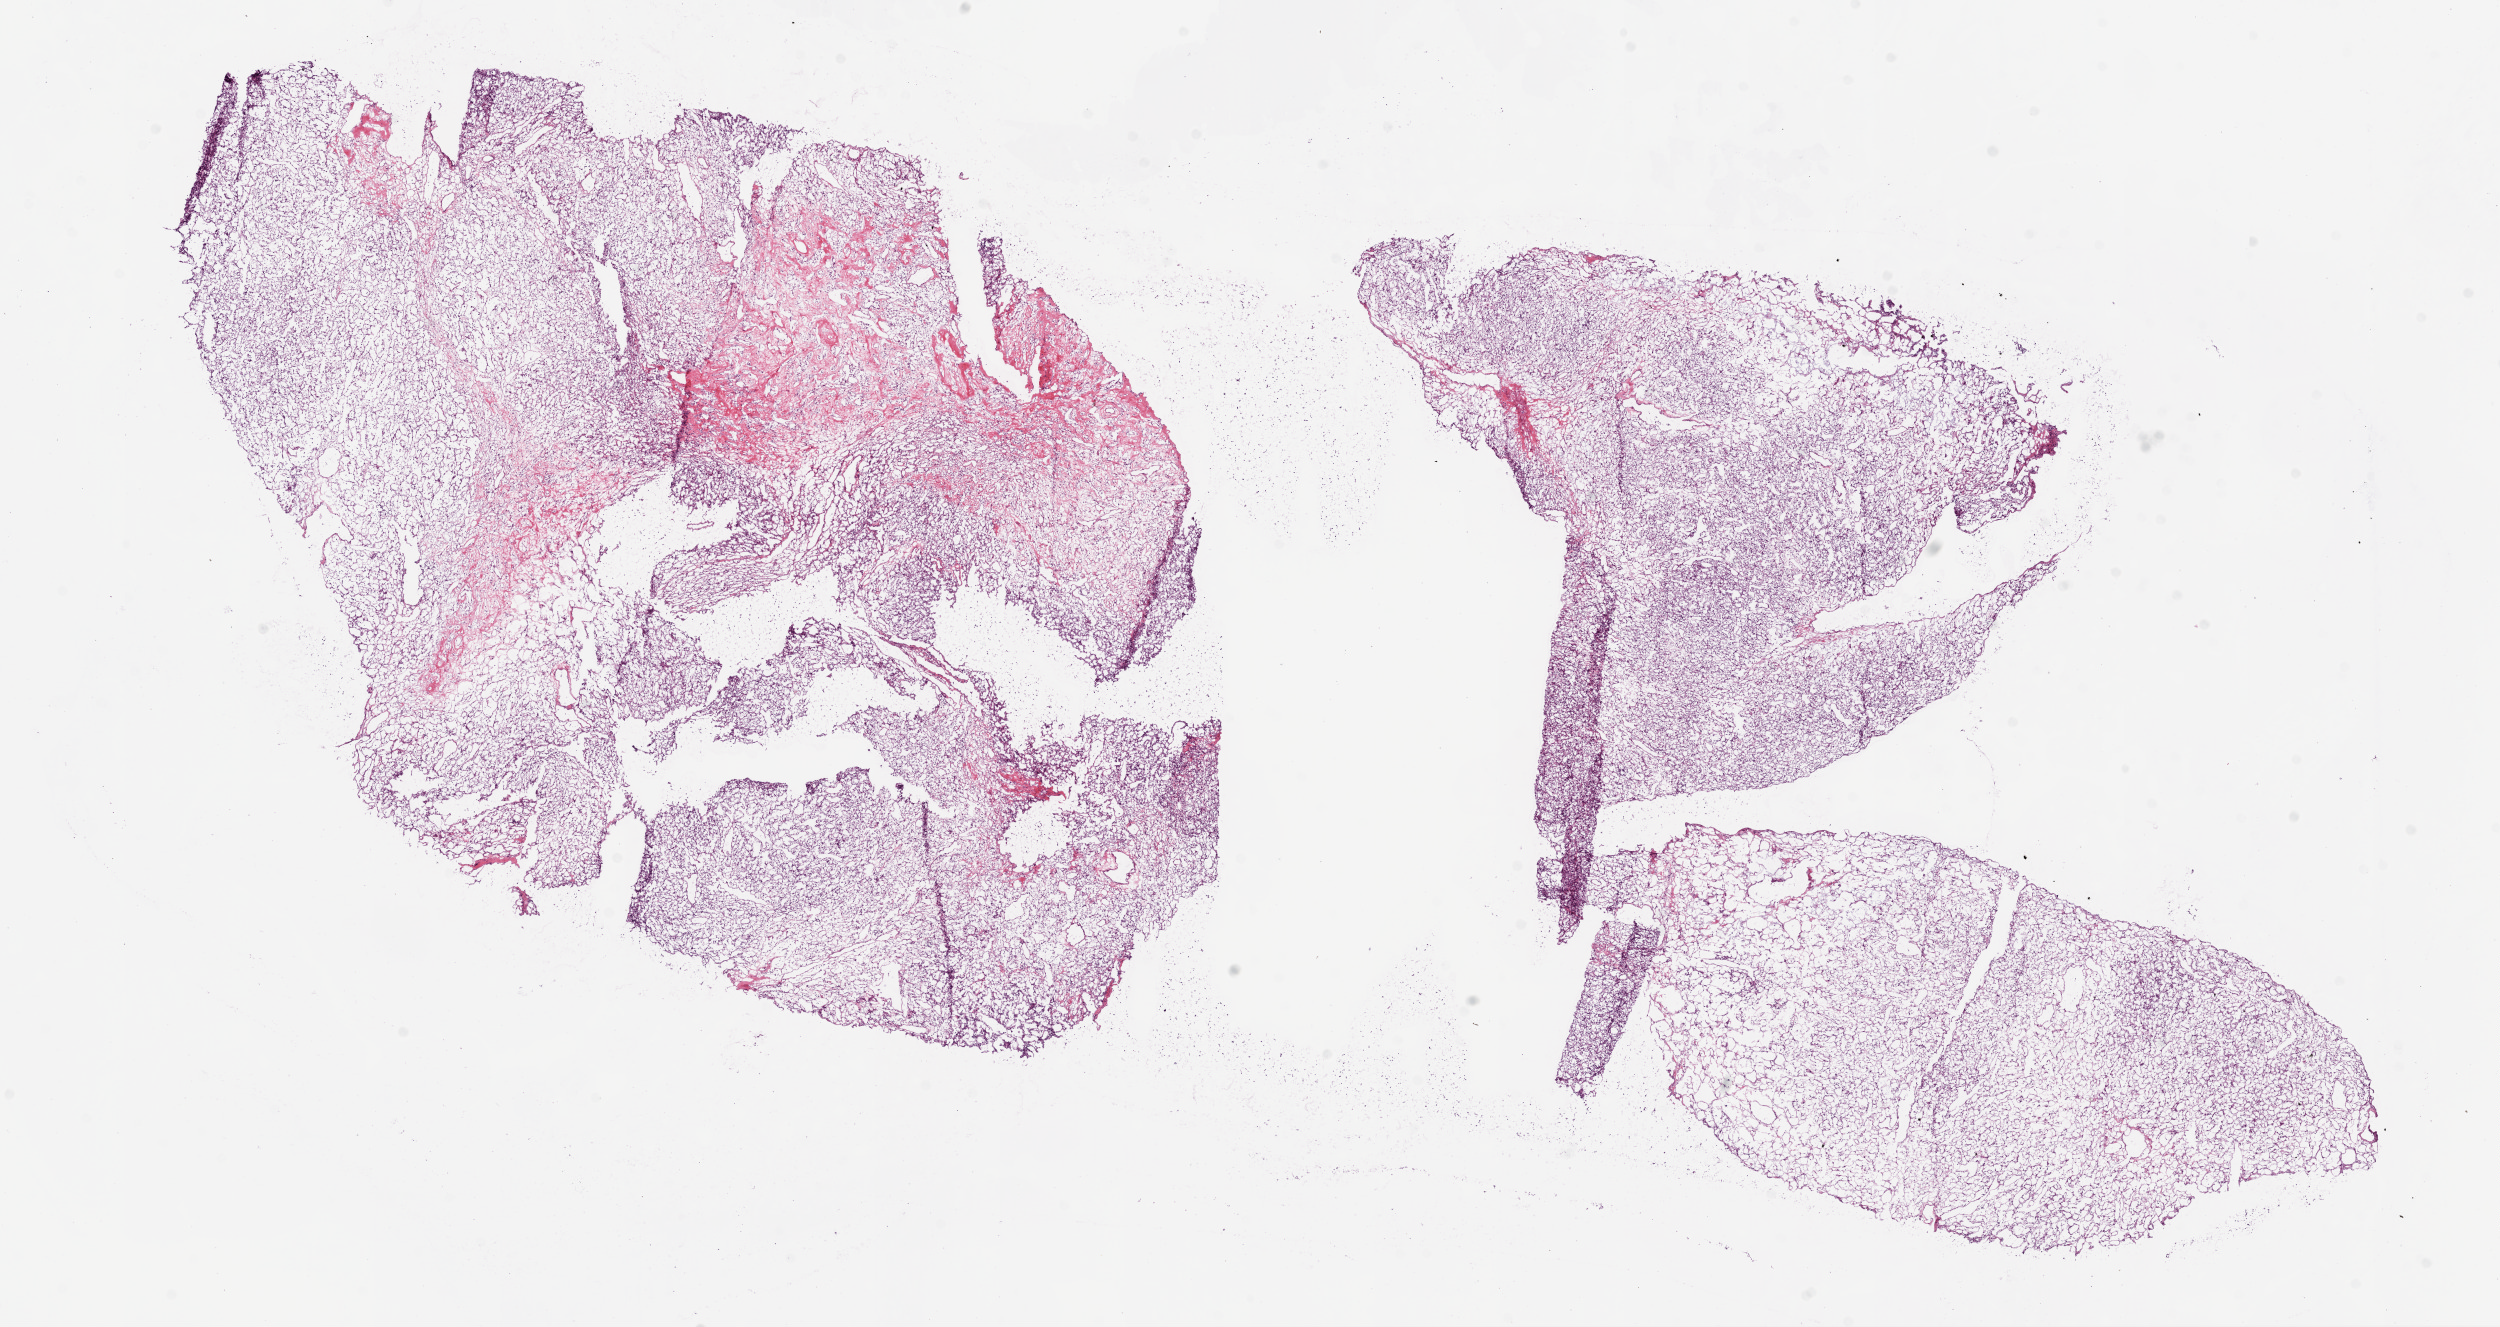
Whole-slide histology image, Hematoxylin and eosin (H&E) stained, a low-resolution overview of the entire scanned area, about 20.1 x 10.6 mm (acquisition: 20x scan). Frozen section from the bottom of the tissue portion. Primary tumour sample from the kidney. Patient: female, age at initial diagnosis 42 years. Histologic grade: G3 (poorly differentiated). Composition of this section per pathologist review: tumour cells 85%, tumour nuclei 85%, normal cells 0%, stromal cells 15%, necrosis 0%.
* pathologic diagnosis: Clear cell adenocarcinoma, NOS
* TNM: T1a NX M0
* AJCC pathologic stage: I
* laterality: left